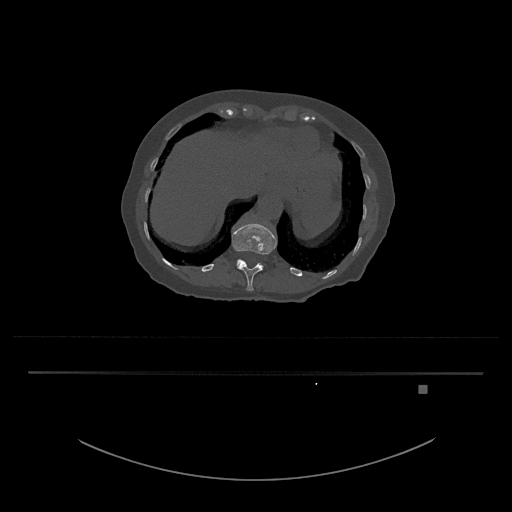
CT including the spine, one axial slice. Slice 600 of 797 in the series (ordered by position). 120 kVp. Bone window (W 1800 / L 400 HU). 512 × 512 image matrix, field of view 500 × 500 mm. Patient: female, 57 years. From the clinical record (not read from this slice): primary cancer: cervical.
Structures marked on this image (semi-automatically segmented with operator editing):
- L1 vertebra: bounding box (x1, y1, x2, y2) in pixels: (237, 260, 262, 265)
- T12 vertebra: (232, 223, 277, 291)